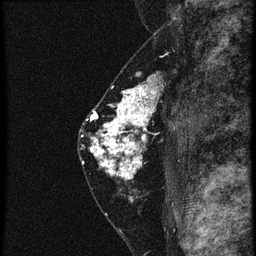
Breast MRI (dynamic contrast-enhanced), one sagittal slice. Slice 35 of 60 in the series (ordered by position). 4 images stored at this slice position (order not interpretable as contrast timing). 1.5 T. TE 4.2 ms, TR 20.4 ms. 1.5 mm slice thickness. 256 × 256 image matrix, field of view 180 × 180 mm. Patient: female, 46 years. From the clinical record (not read from this slice): setting: breast cancer imaged before/during neoadjuvant chemotherapy; receptor status: triple-negative.
Outlined on this slice (semi-automatic segmentation, software-assisted and operator-edited):
- analysis volume of interest (the breast-tissue region the enhancement analysis was run in; not a lesion): bounding box (x1, y1, x2, y2) in pixels: (88, 82, 177, 185)
- tumour enhancement mask (voxels above the 90 % enhancement threshold inside the analysis volume of interest): (90, 82, 163, 179)